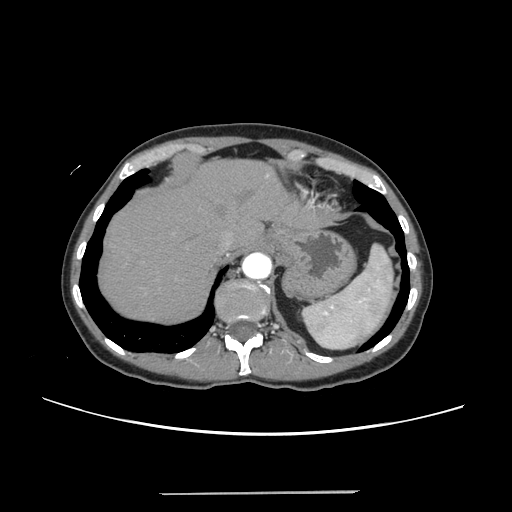
Contrast-enhanced abdominal CT, one axial slice; slice 202 of 240 in the series (ordered by position); 120 kVp; intravenous contrast given; soft-tissue window (W 400 / L 40 HU); 1.25 mm slice thickness; 512 × 512 image matrix, field of view 371 × 371 mm. Female patient, age 60 years. From the clinical record (not read from this slice): diagnosis: colorectal cancer liver metastases, imaged before liver resection; multiple liver metastases: no; largest metastasis: 1.5 cm; disease in both lobes: no.
Outlined on this slice (manually delineated by an expert):
- hepatic veins: bounding box <220,218,250,251> (left, top, right, bottom; pixels)
- liver: <99,160,318,322>
- planned liver remnant (the part of the liver to remain after resection): <99,160,312,322>